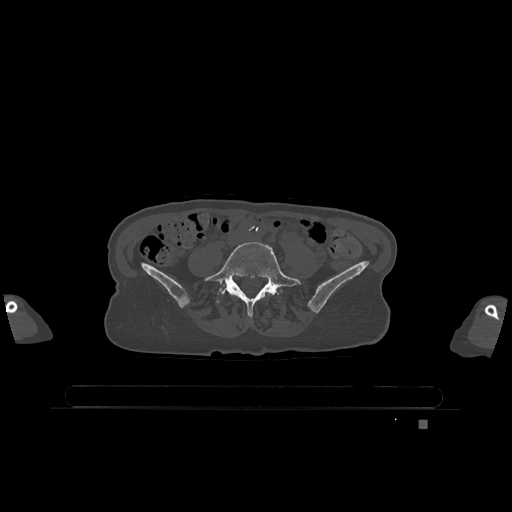
CT including the spine, one axial slice. Slice 245 of 1317 in the series (ordered by position). Bone window (W 1800 / L 400 HU). 0.5 mm slice thickness. 512 × 512 image matrix, field of view 500 × 500 mm. Female patient, age 74 years. Case-level facts recorded for this patient, not image findings: primary cancer: lung; vertebrae with lytic lesions (as recorded): T1, T4, T5, T6, L4, L5.
Outlined on this slice (semi-automatic segmentation, software-assisted and operator-edited):
- L5 vertebra: box from (x=204, y=242) to (x=301, y=316) px